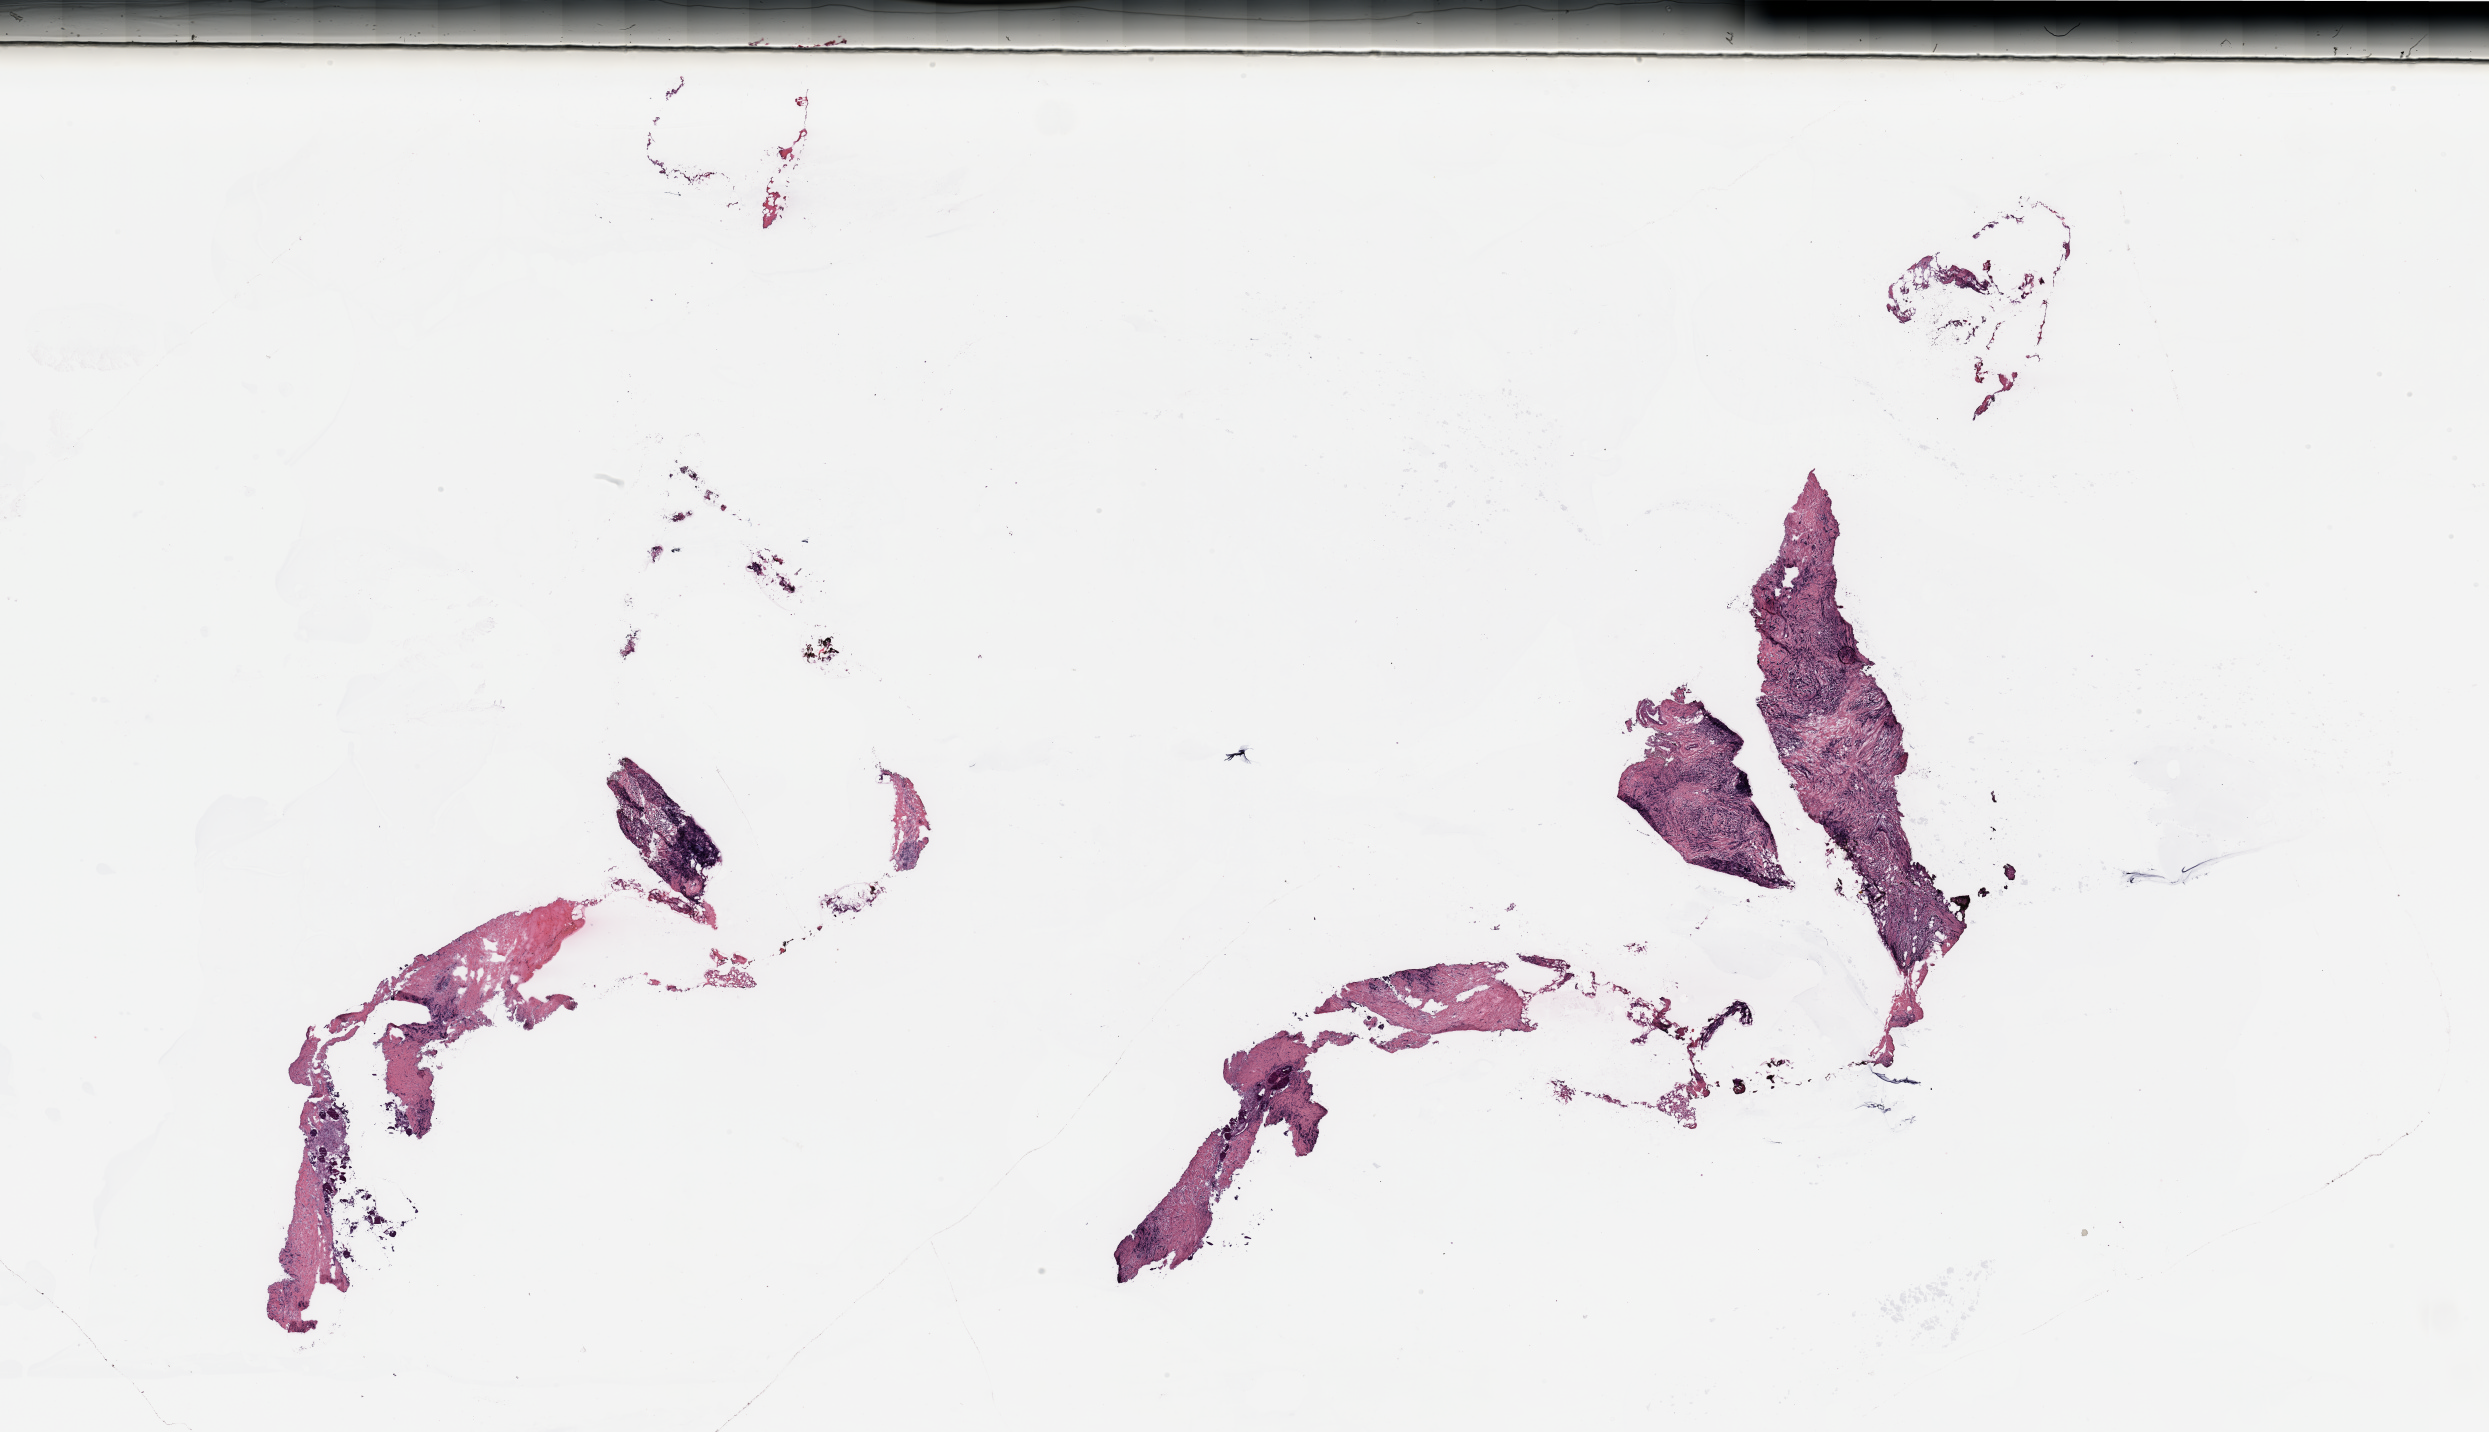
Digitized H&E tissue section (whole slide) — shown as a low-resolution overview of the whole scanned area (about 39.4 x 22.7 mm). Breast, tissue type not recorded.
- patient diagnosis (cohort enrolment): breast cancer (breast)